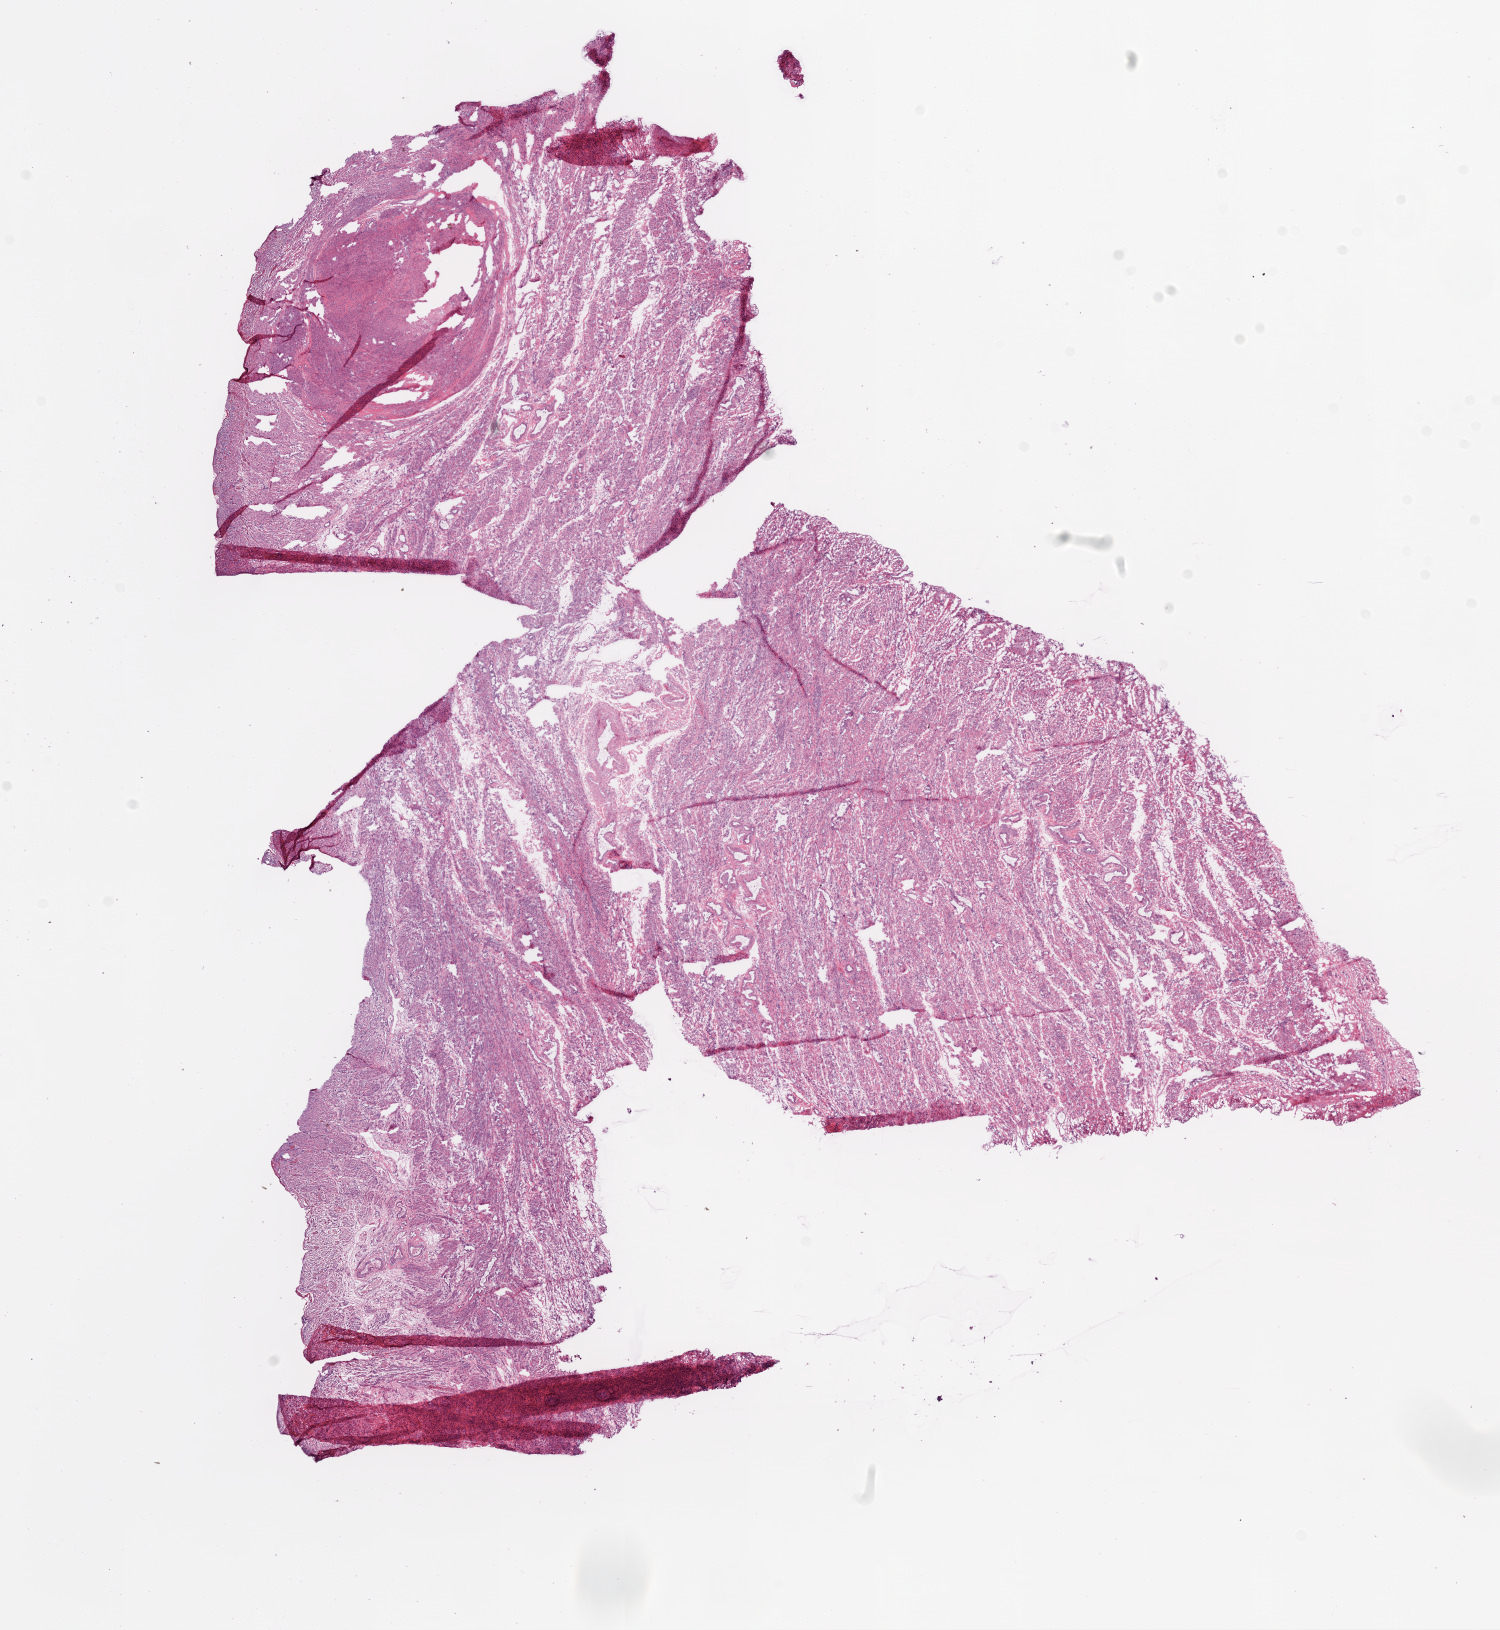
Digitized H&E-stained tissue section (whole slide) — a low-resolution overview of the entire scanned area, about 12.0 x 13.1 mm. Frozen section from the bottom of the tissue portion. Ovary, solid tissue normal (non-tumour tissue) sample. Female, age 63 years at initial diagnosis.
This section: solid tissue normal (non-tumour) sample from the same patient. Patient diagnosis: Serous cystadenocarcinoma, NOS.